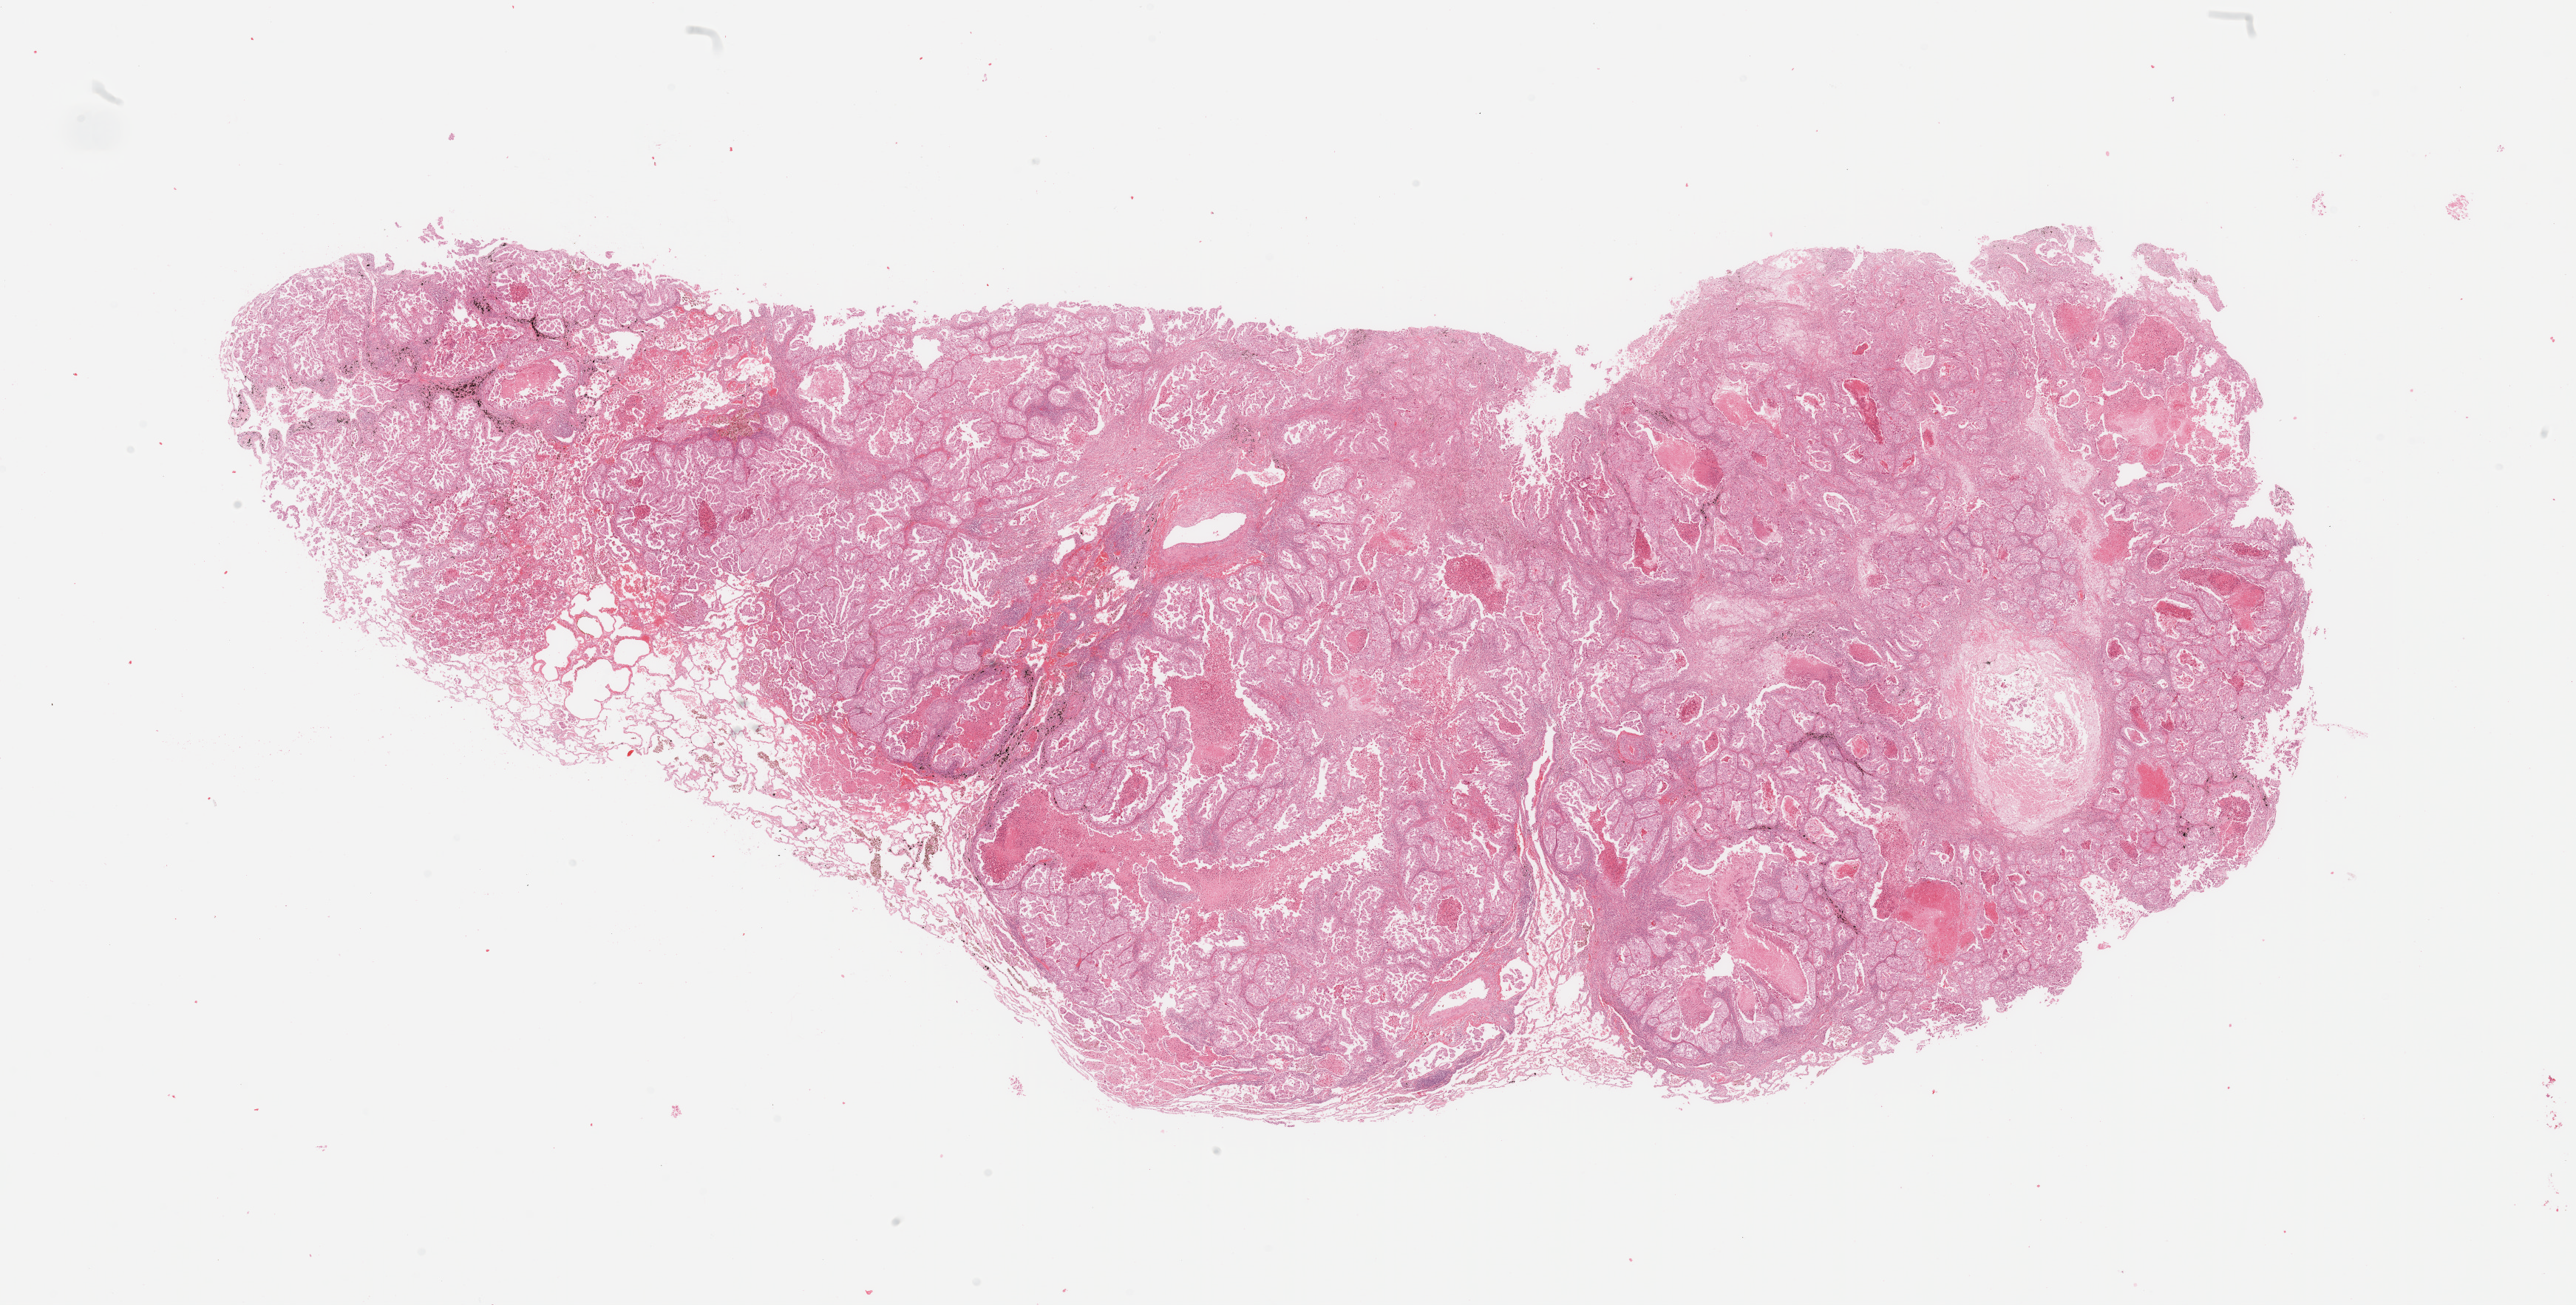
Hematoxylin and eosin (H&E) stained whole-slide image — a low-resolution overview of the entire scanned area, about 27.6 x 14.0 mm, tumour tissue sample, sampled site: lung. Patient: male, age 48 years. Histologic grade: G2 (moderately differentiated). Composition of this section per pathologist review: tumour nuclei 80%, necrosis 5%.
AJCC pathologic stage: IB. Histologic diagnosis: Adenocarcinoma, NOS. Primary tumour site (as recorded): right lower lobe.